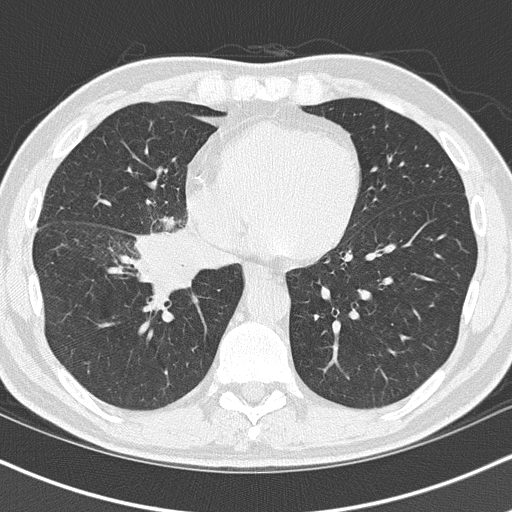
Axial slice from a low-dose chest CT screening exam, first (baseline) screen, lung window (W 1500 / L -600 HU), 2 mm slice thickness, slice 48 of 151 in the series. Male participant, aged 55 years at enrolment. Current smoker at enrolment.
Expert-annotated lung lesion, bounding box [x1, y1, x2, y2] px = [128, 224, 242, 310]. Screening reader's record for this exam (one nodule recorded; not confirmed to be the boxed lesion): non-calcified nodule or mass ≥4 mm, right lower lobe, 6 × 5 mm, spiculated (stellate) margins, soft tissue attenuation. Participant outcome: lung cancer diagnosed 21 days after this screen — carcinoma, NOS, right hilum, stage IB (AJCC 6th edition), 67 mm at pathology.